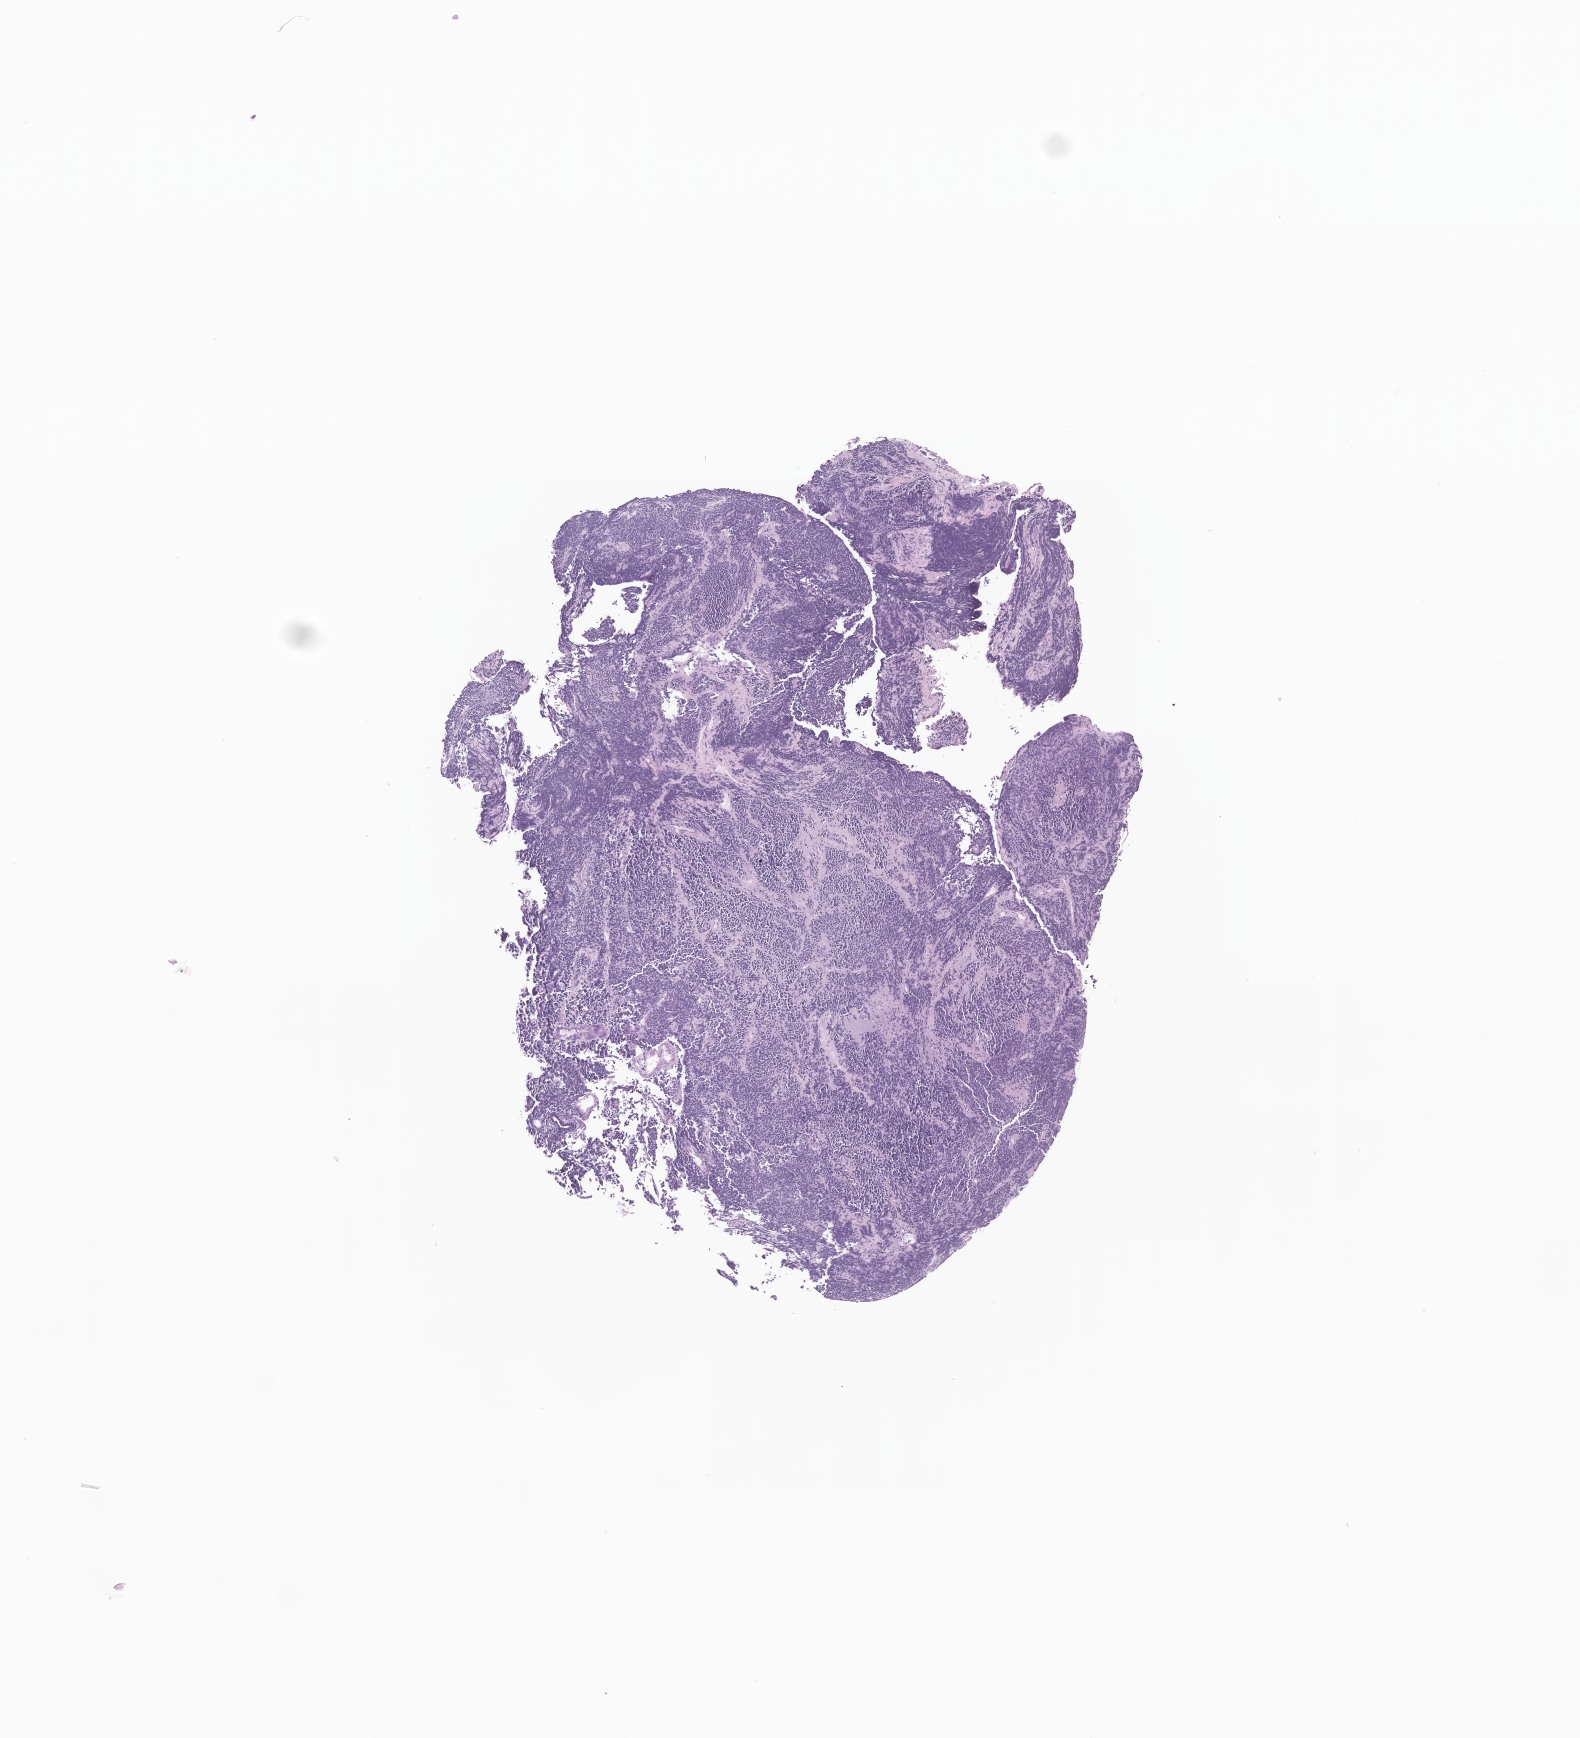
Digitized H&E-stained section of tumor tissue from the pineal gland — low-resolution overview of the scanned area, about 6.7 x 7.3 mm; formalin-fixed paraffin-embedded section. Patient: female, age 251 months (20 years 11 months).
* diagnosis (ICD-O-3 morphology term): Pineoblastoma